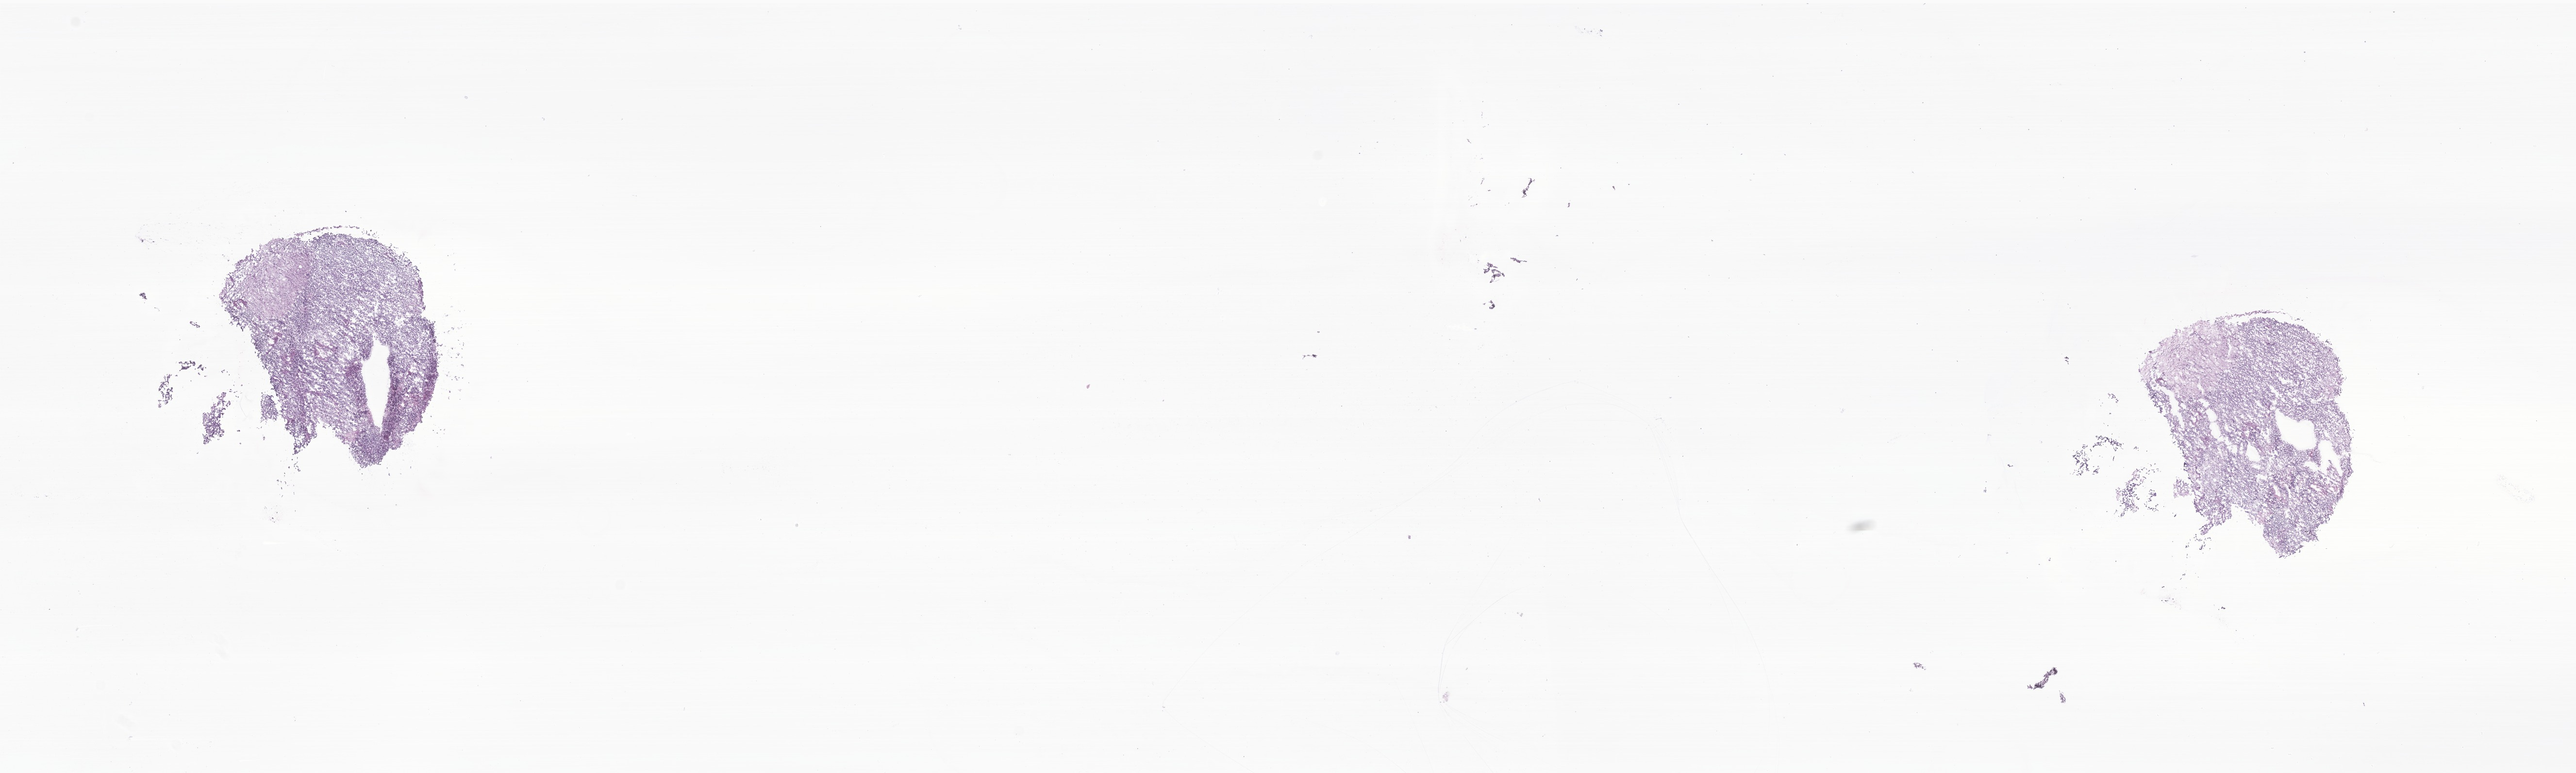
Whole-slide image, haematoxylin and eosin stain of tumor tissue from the pineal gland, whole scanned area (about 22.4 x 6.7 mm) shown as a low-resolution overview; frozen section. Female patient, age 631 days (about 1.7 years).
Diagnosis: Atypical teratoid/rhabdoid tumor.